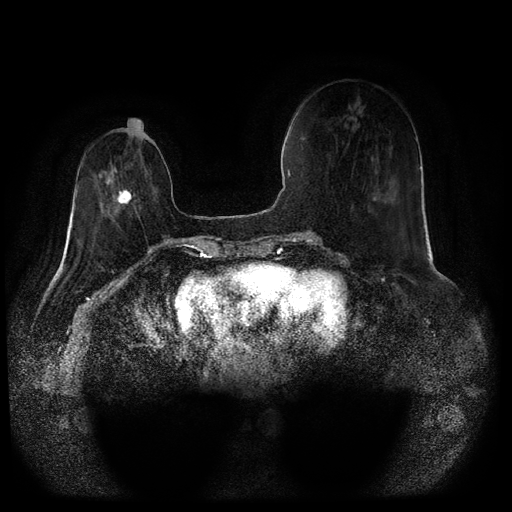
Breast MRI (dynamic contrast-enhanced, multi-phase), one axial slice; slice 26 of 116 in the series (ordered by position); dynamic contrast-enhanced series, time point 2 of 5 at this slice position (early post-contrast); 1.5 T; TE 2.6 ms, TR 5.3 ms; 2 mm slice thickness; 512 × 512 image matrix, field of view 360 × 360 mm. Patient: female, 71 years.
Outlined on this slice (semi-automatically segmented with operator editing):
- breast lesion (labelled 'tumour' in the annotation; benign lesions carry a separate 'benign' label): box from (x=115, y=188) to (x=135, y=205) px